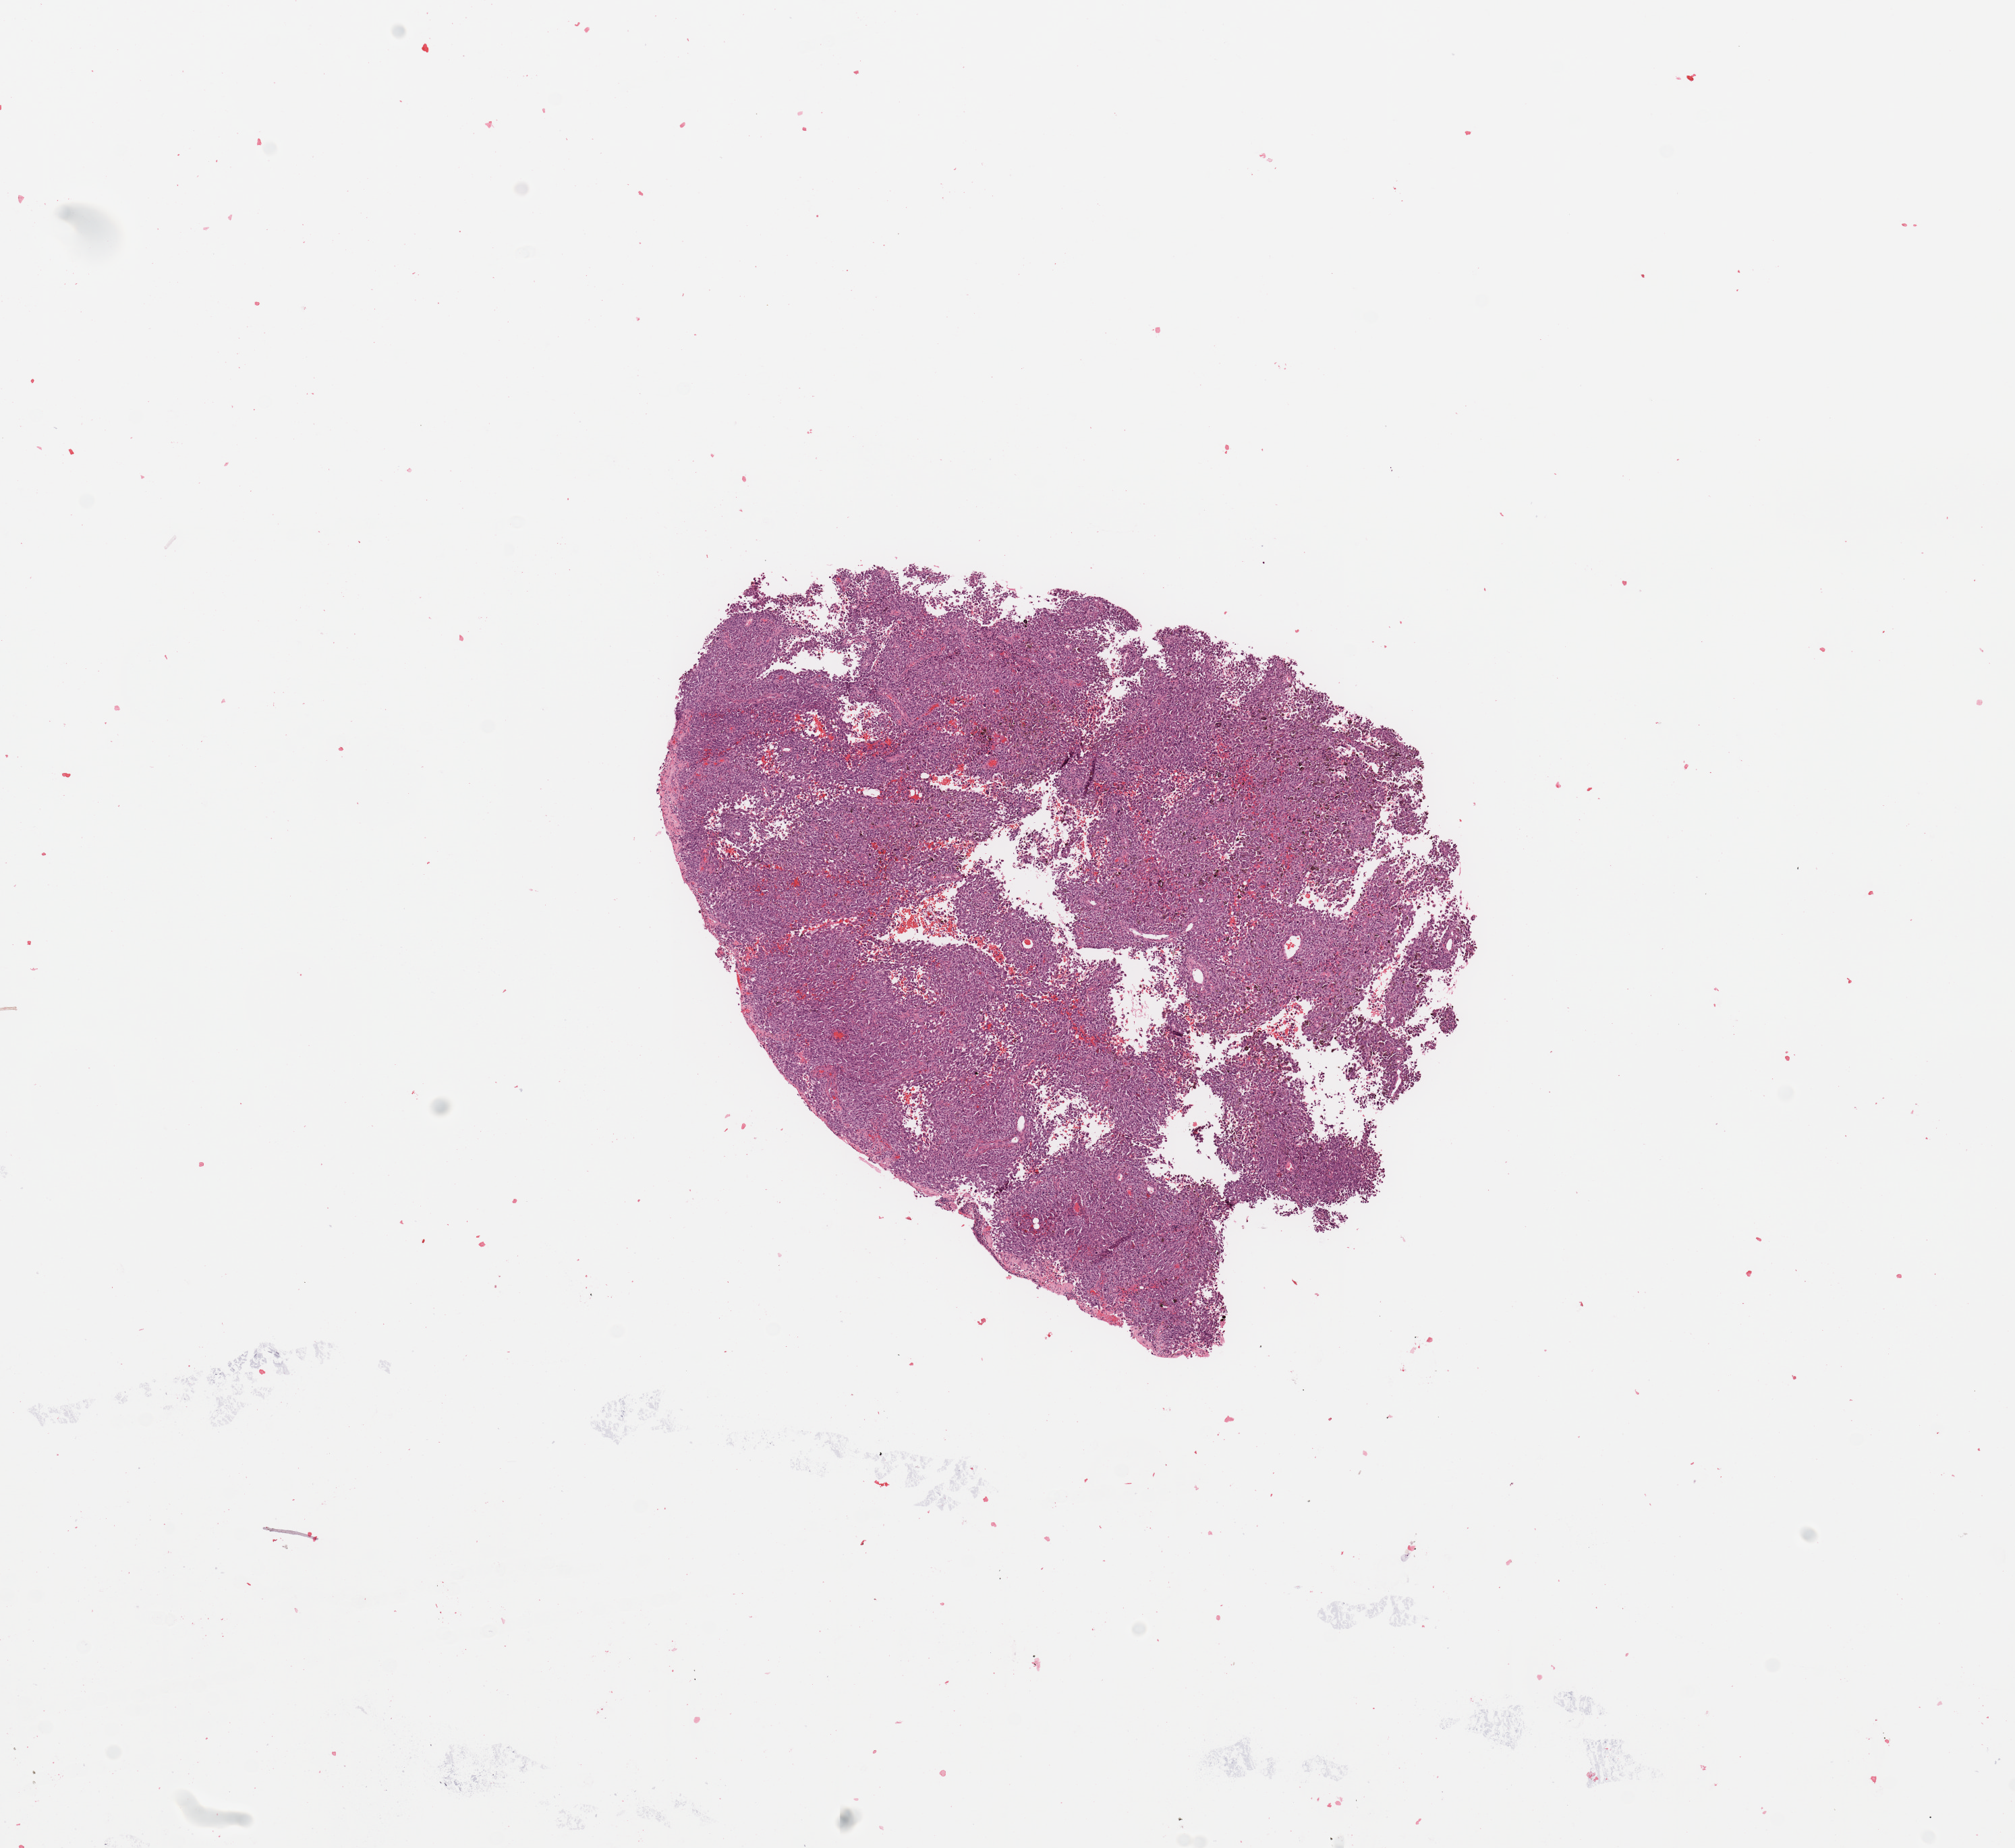
Whole-slide histology image, H&E, whole scanned area (about 11.8 x 10.8 mm, slide scanned at 20x) shown as a low-resolution overview, tumour tissue sample, sampled site: trunk. Patient: male, age 34 years. Pathologist review of this section (percent, as recorded): tumour nuclei 99%, necrosis 0%.
- this section: metastatic tumour tissue
- patient diagnosis: Malignant melanoma, NOS